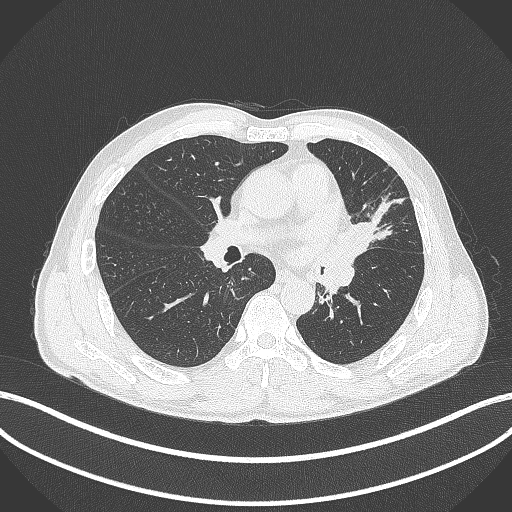
Chest CT, one axial slice; slice 227 of 429 in the series (ordered by position); reconstruction kernel B70f; 120 kVp; lung window (W 1500 / L -600 HU); 1 mm slice thickness; 512 × 512 image matrix. Male patient, age 57 years. From the clinical record (not read from this slice): clinical TNM (as recorded): T2b N0 M0.
Structures marked on this image (bounding box drawn by a radiologist):
- lung tumour (recorded histology: squamous cell carcinoma): bounding box [x1, y1, x2, y2] px = [331, 213, 372, 270]